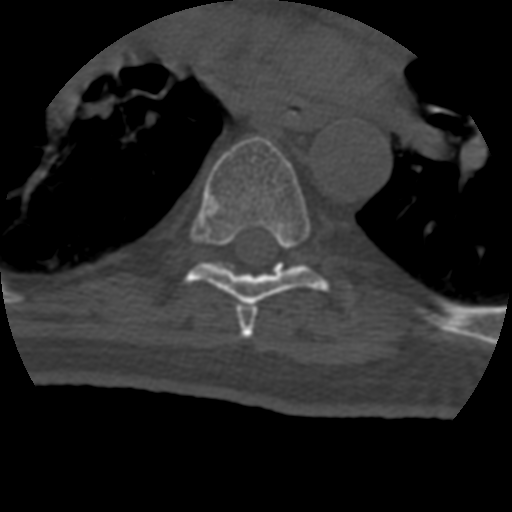
CT including the spine, one axial slice. Position 280 of 399 along the scan axis. Reconstruction kernel STANDARD. 120 kVp. Bone window (W 1800 / L 400 HU). 1.25 mm slice thickness. 512 × 512 image matrix, field of view 160 × 160 mm. Patient age 69 years. From the clinical record (not read from this slice): primary cancer: prostate.
Annotated regions visible in this slice (semi-automatically segmented with operator editing):
- T6 vertebra: bounding box [x1, y1, x2, y2] px = [236, 305, 257, 339]
- T7 vertebra: [186, 137, 329, 305]